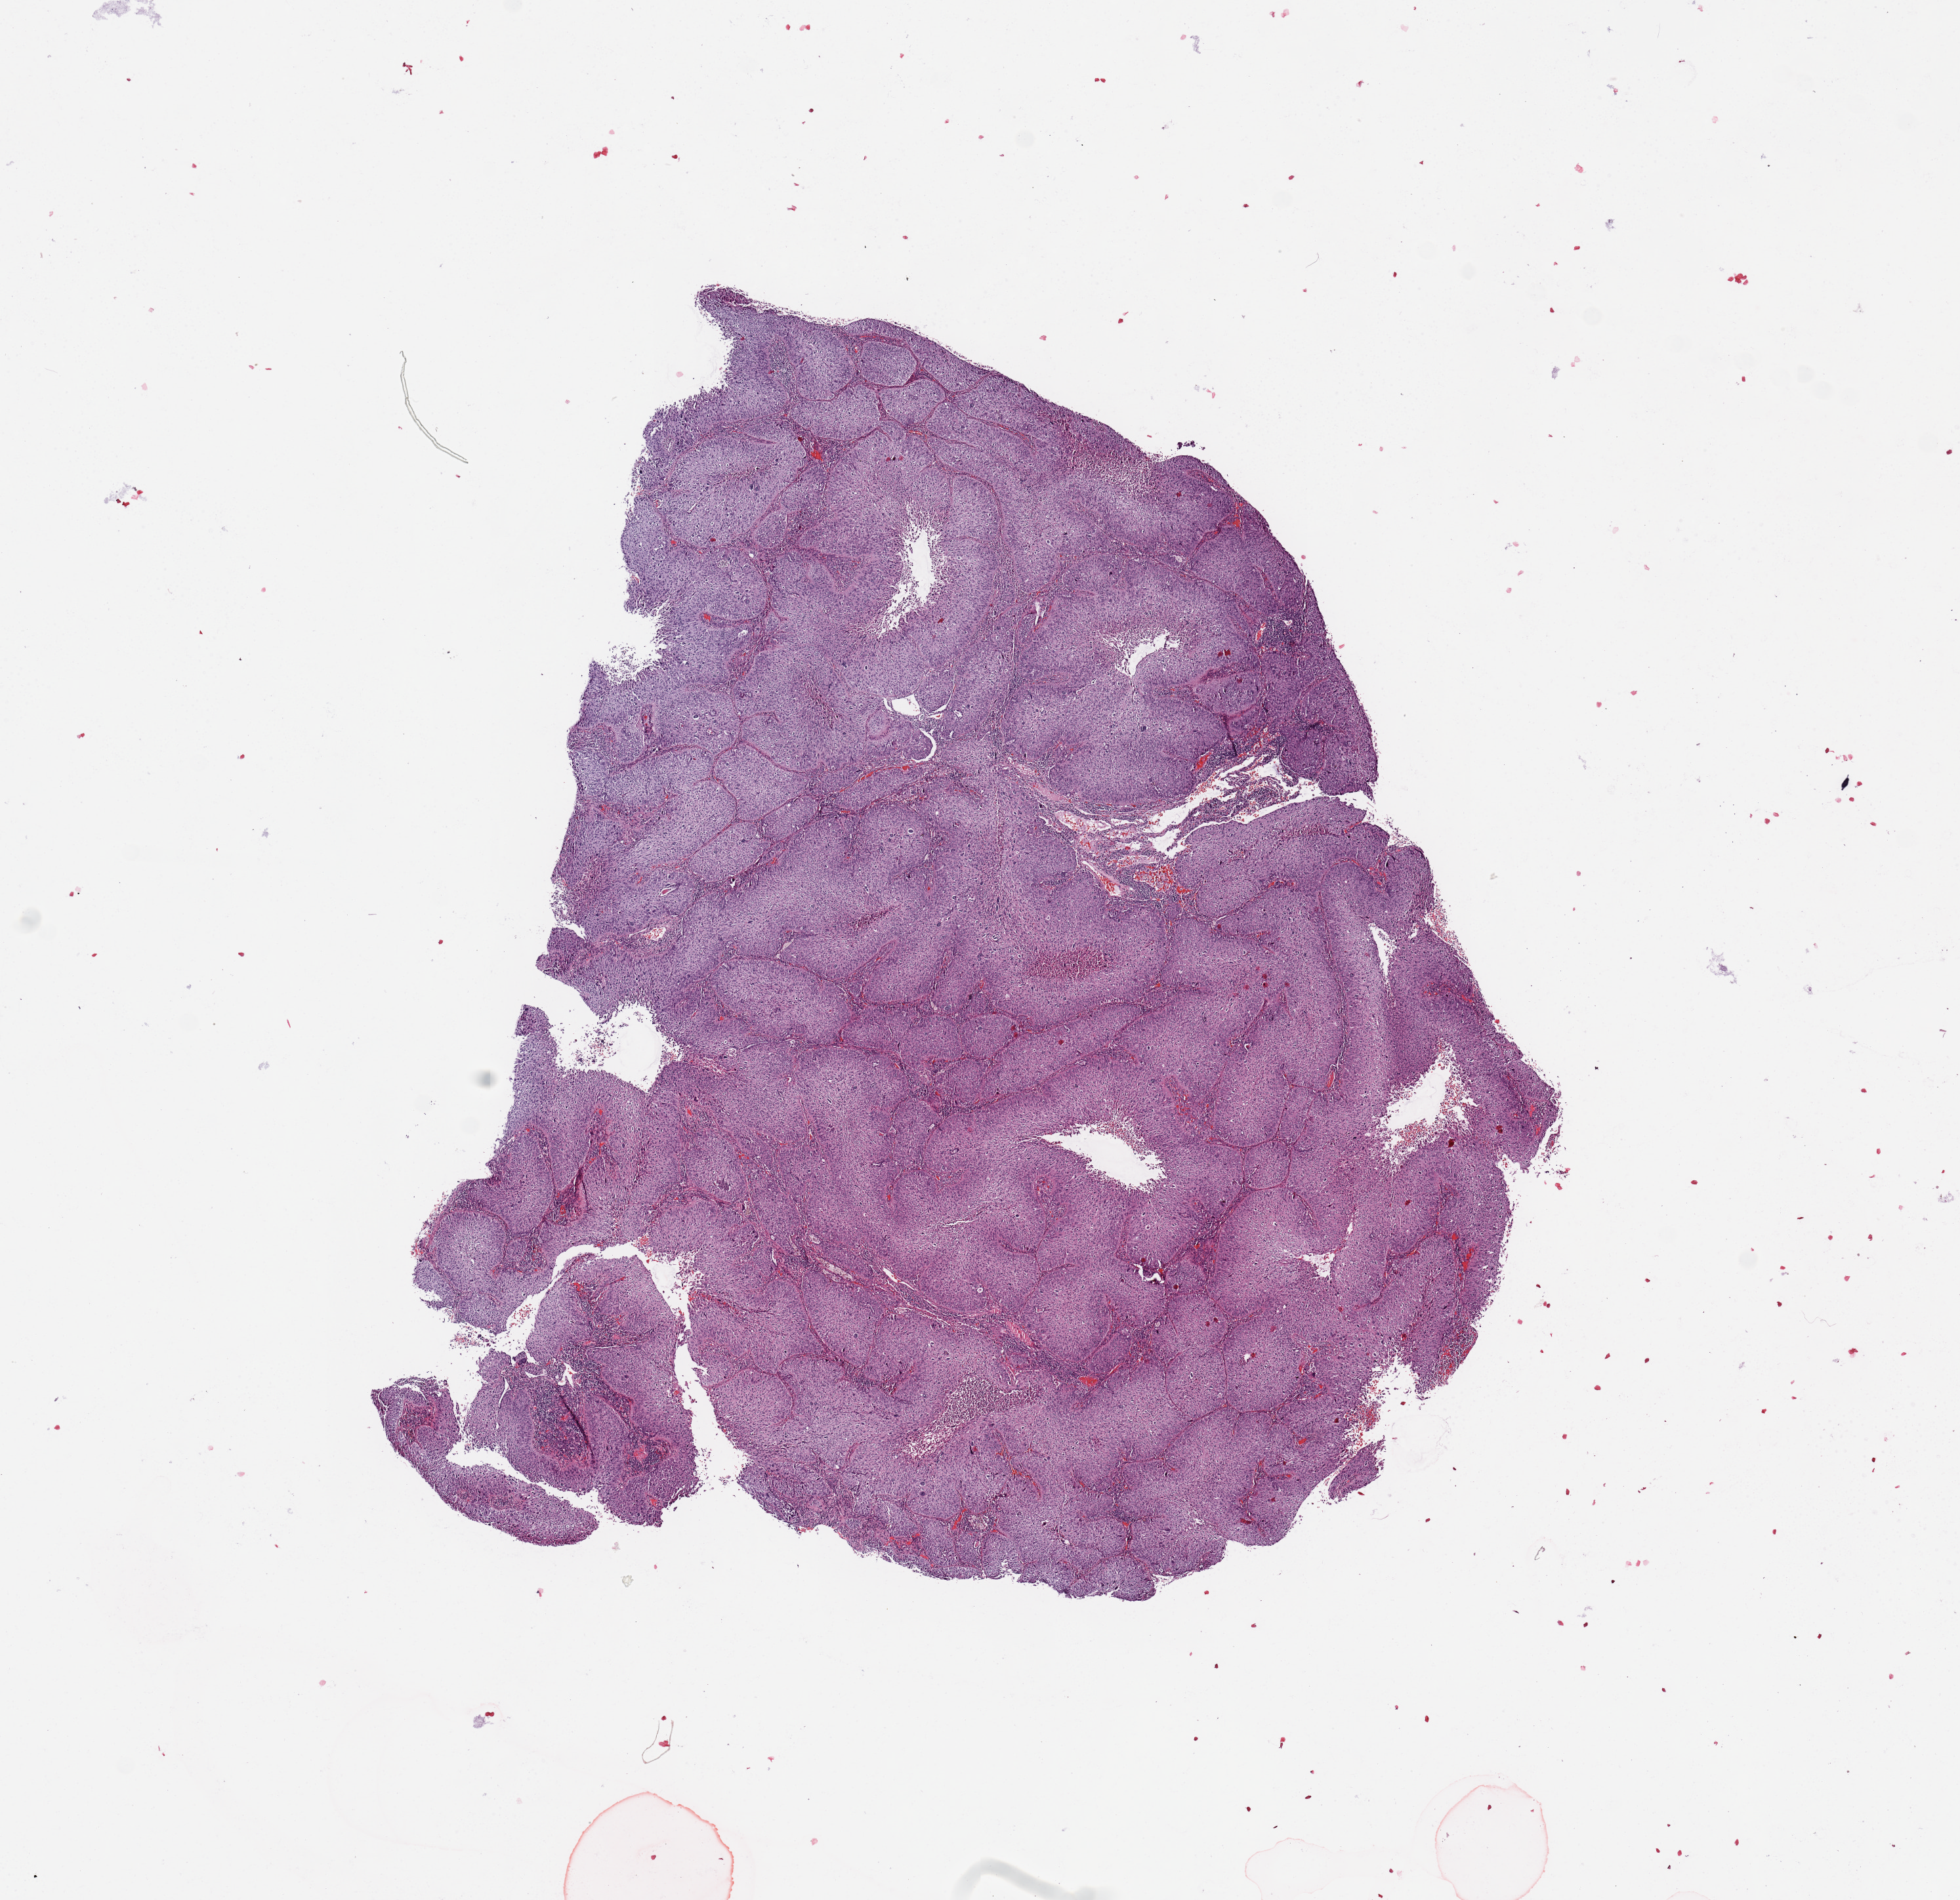
Whole-slide histology image, Hematoxylin and eosin (H&E) stained — shown as a low-resolution overview of the whole scanned area (about 11.8 x 11.5 mm). Tumour tissue sample, sampled site: lung. Patient: female, age 64 years. Histologic grade: G3 (poorly differentiated). Slide review estimates, as recorded: tumour nuclei 85%, necrosis 3%.
Diagnosis: Squamous cell carcinoma, NOS. Primary tumour site (as recorded): right lower lobe. AJCC pathologic stage: IA.